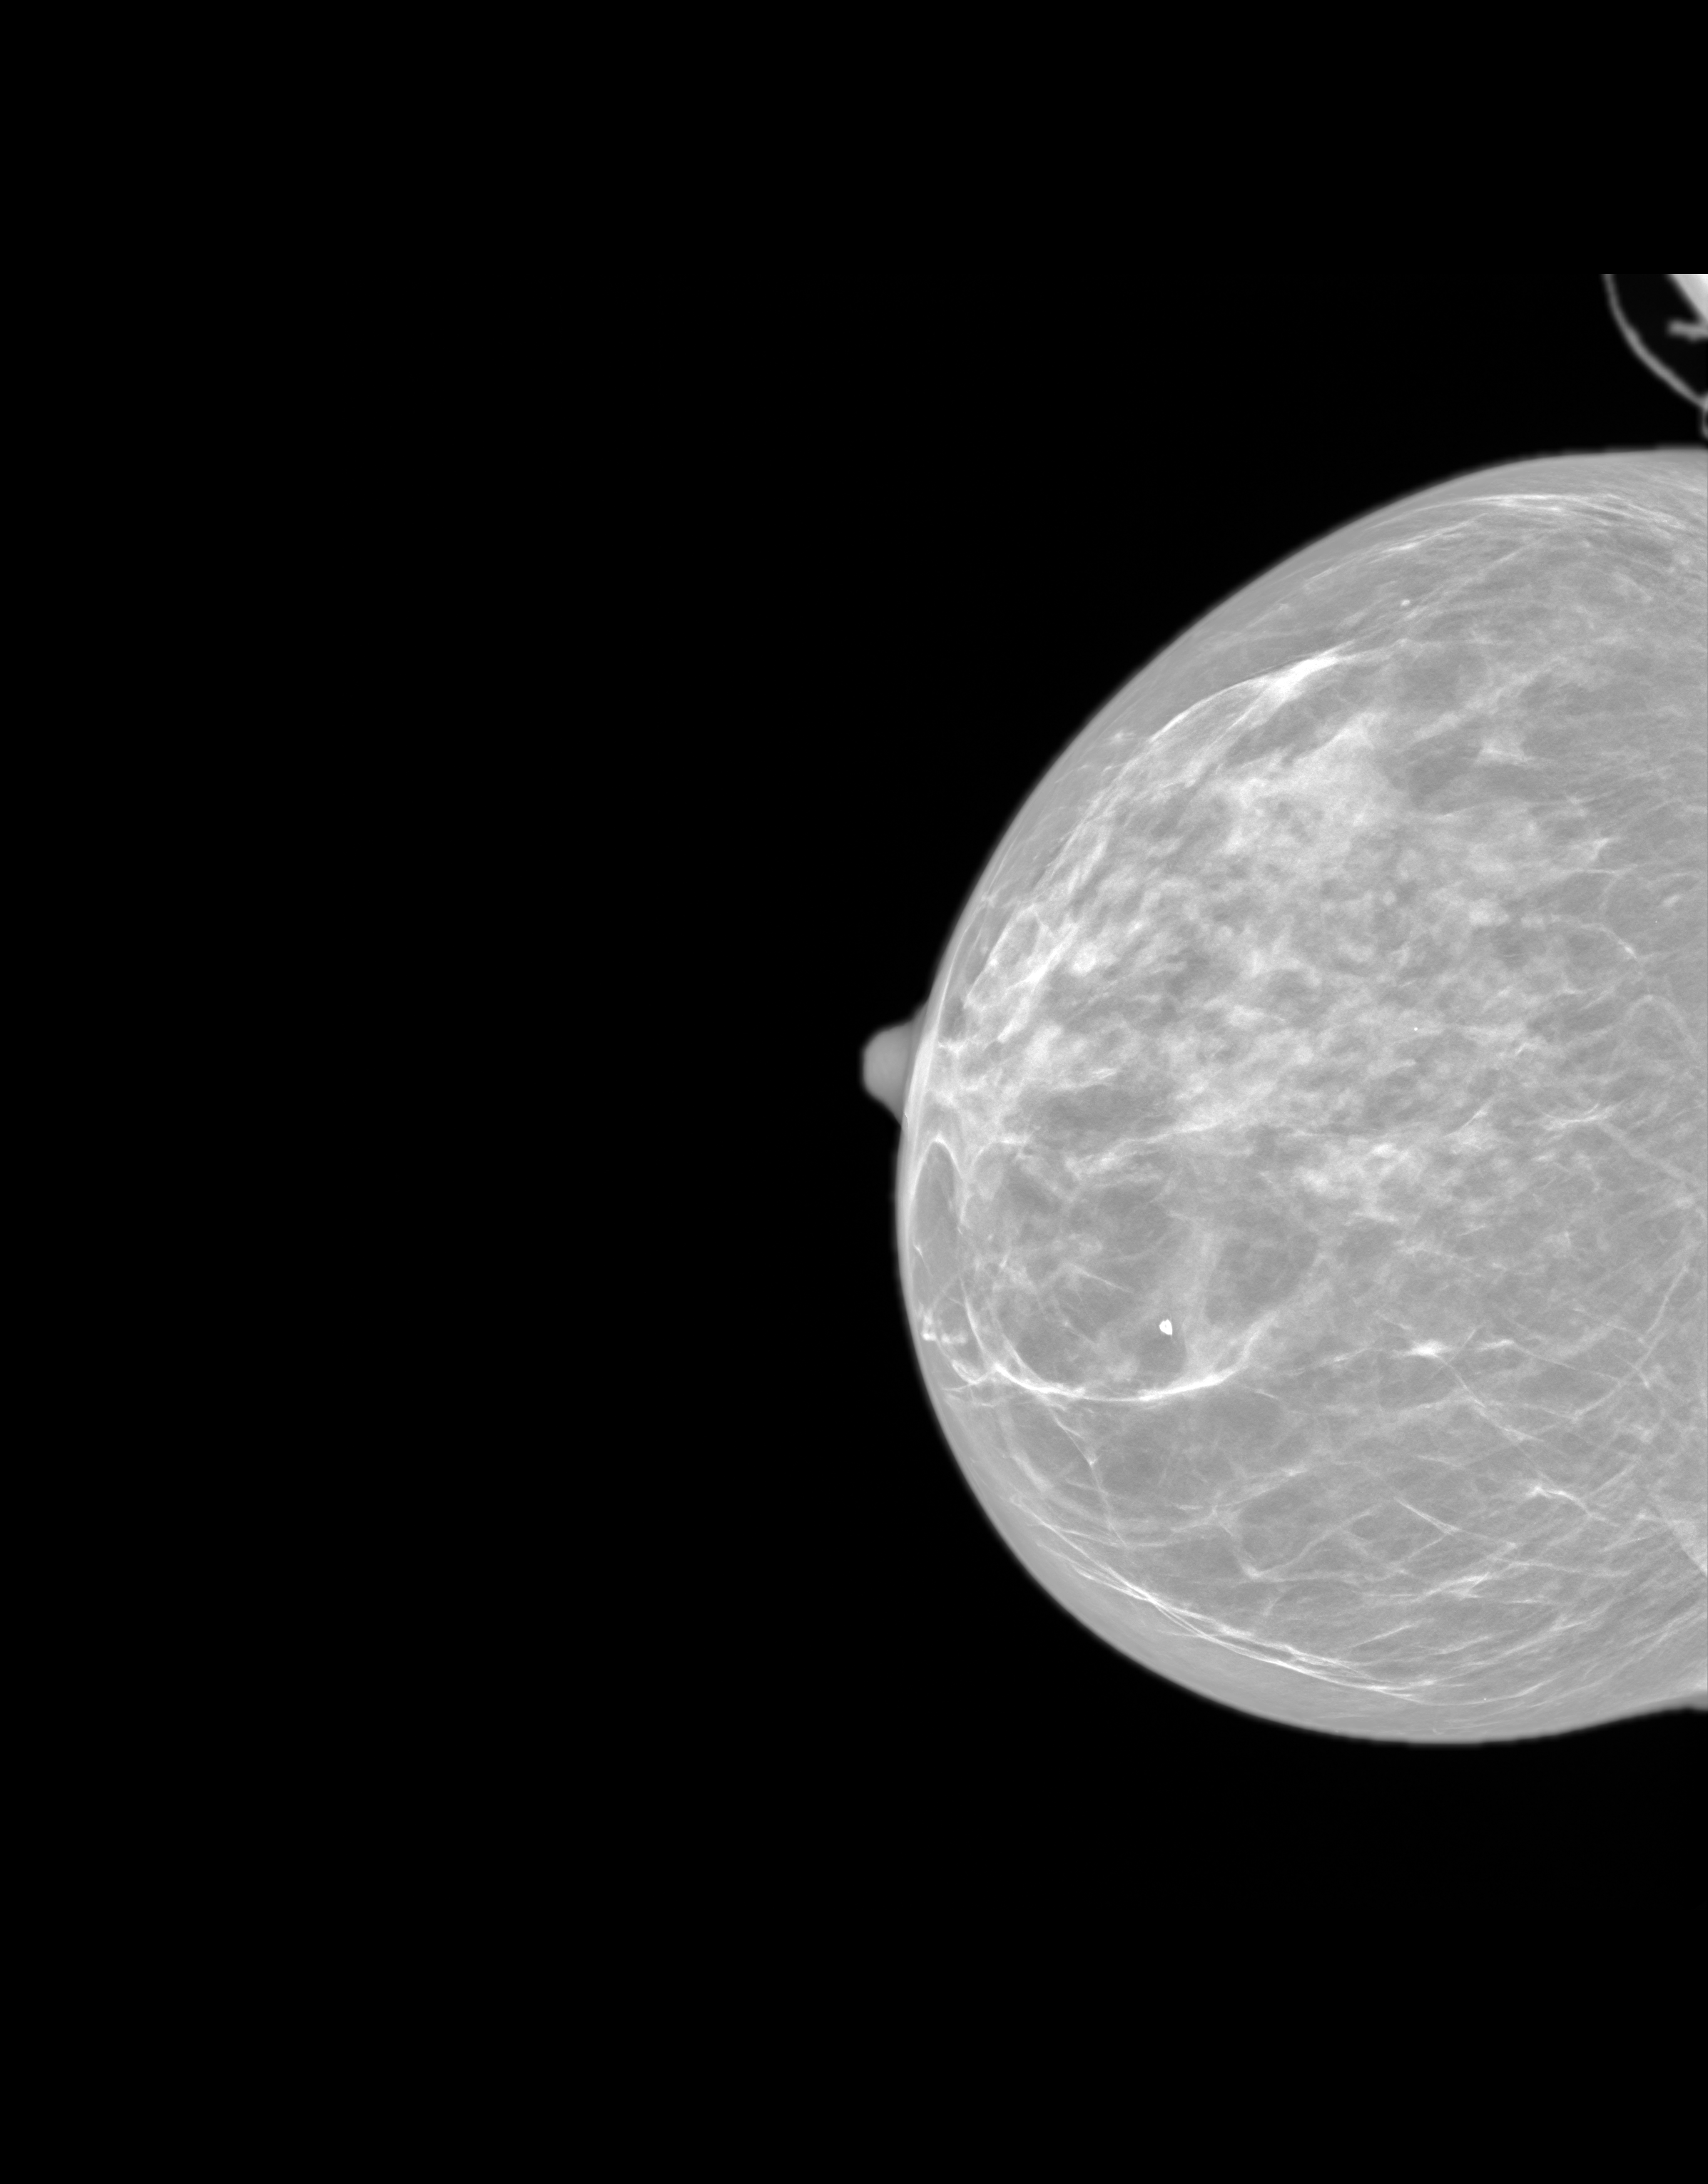
Synthetic 2-D view generated from a tomosynthesis acquisition (not an FFDM exposure), right breast, cranio-caudal projection, annual screening mammography examination, system: SenoIris_1SP1.1(421). Female patient, age 56 years.
BI-RADS breast density category at the screening exam (both breasts, scale 1–4): 3. Final BI-RADS category for the screening round (tomosynthesis exam, both breasts): category 1. Recall: no recall after this screen.